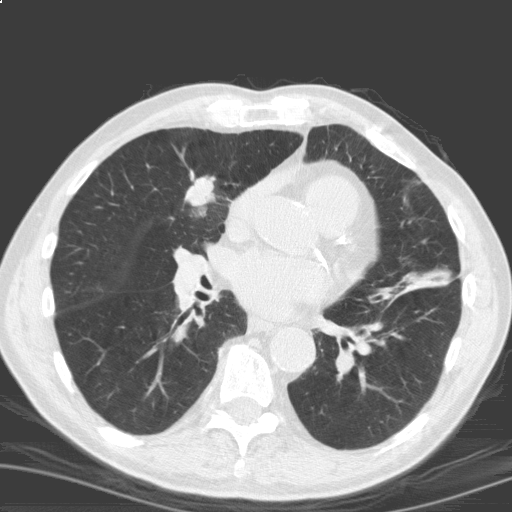
Chest CT (low-dose screening protocol), one axial image. Second annual screen. Lung window (W 1500 / L -600 HU). 3.2 mm slice thickness. Male, age 69 years at enrolment. Current smoker at enrolment.
Expert reader's lesion annotation, bounding box <168,161,233,224> (left, top, right, bottom; pixels). The screening reader recorded 2 non-calcified nodules or masses ≥4 mm on this exam; which of them this box marks is not recorded. Official screen result: positive, other.